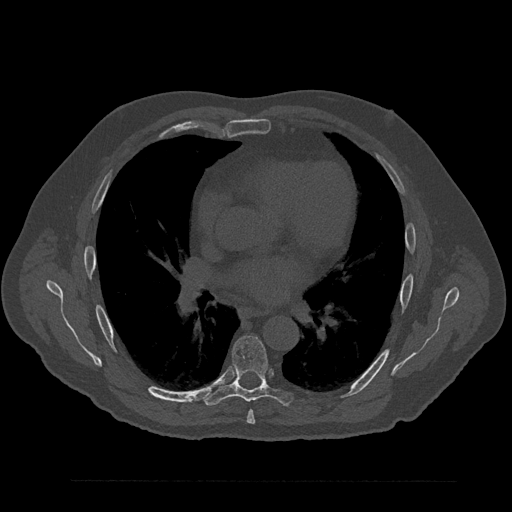
CT including the spine, one axial slice. Slice 514 of 797 in the series (ordered by position). 120 kVp. Bone window (W 1800 / L 400 HU). 512 × 512 image matrix. Male patient, age 61 years. Case-level facts recorded for this patient, not image findings: primary cancer: prostate.
Outlined on this slice (semi-automatic segmentation, software-assisted and operator-edited):
- T6 vertebra: bounding box (x1, y1, x2, y2) in pixels: (247, 410, 256, 424)
- T7 vertebra: (204, 335, 293, 406)